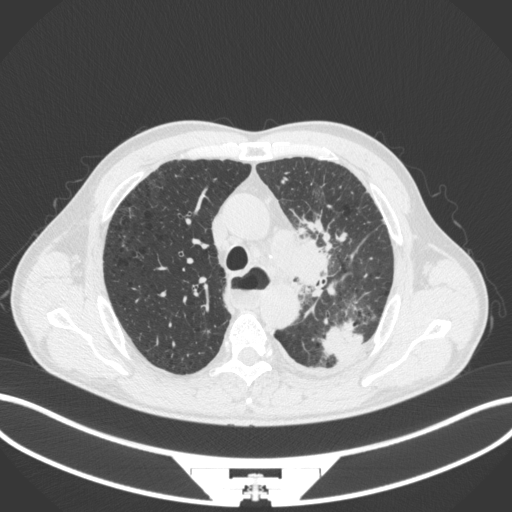
Chest CT, one axial slice; position 278 of 411 along the scan axis; reconstruction kernel B31f; 120 kVp; lung window (W 1500 / L -600 HU); 1 mm slice thickness; 512 × 512 image matrix, field of view 400 × 400 mm. Patient: male, 57 years. From the clinical record (not read from this slice): clinical TNM (as recorded): T2a N1 M0.
Structures marked on this image (rectangle marked by the reading radiologist):
- lung tumour (recorded histology: squamous cell carcinoma): bounding box [x1, y1, x2, y2] px = [269, 230, 343, 286]